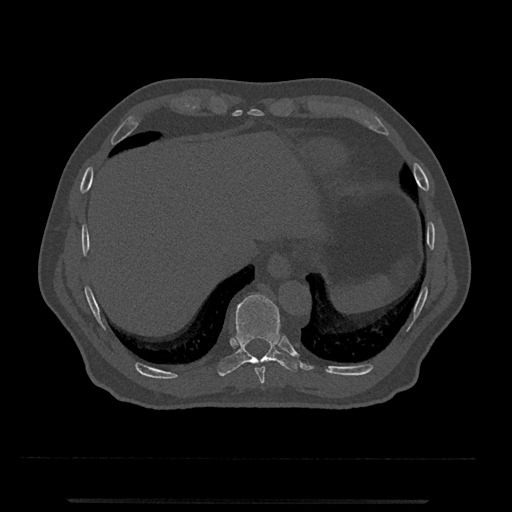
CT including the spine, one axial slice. Slice 533 of 797 in the series (ordered by position). Reconstruction kernel Br40s/3. Bone window (W 1800 / L 400 HU). 0.5 mm slice thickness. 512 × 512 image matrix, field of view 419 × 419 mm. Male patient, age 63 years. Case-level facts recorded for this patient, not image findings: primary cancer: prostate.
Outlined on this slice (semi-automatic segmentation, software-assisted and operator-edited):
- T10 vertebra: bounding box (x1, y1, x2, y2) in pixels: (217, 294, 300, 377)
- T9 vertebra: (255, 367, 265, 384)